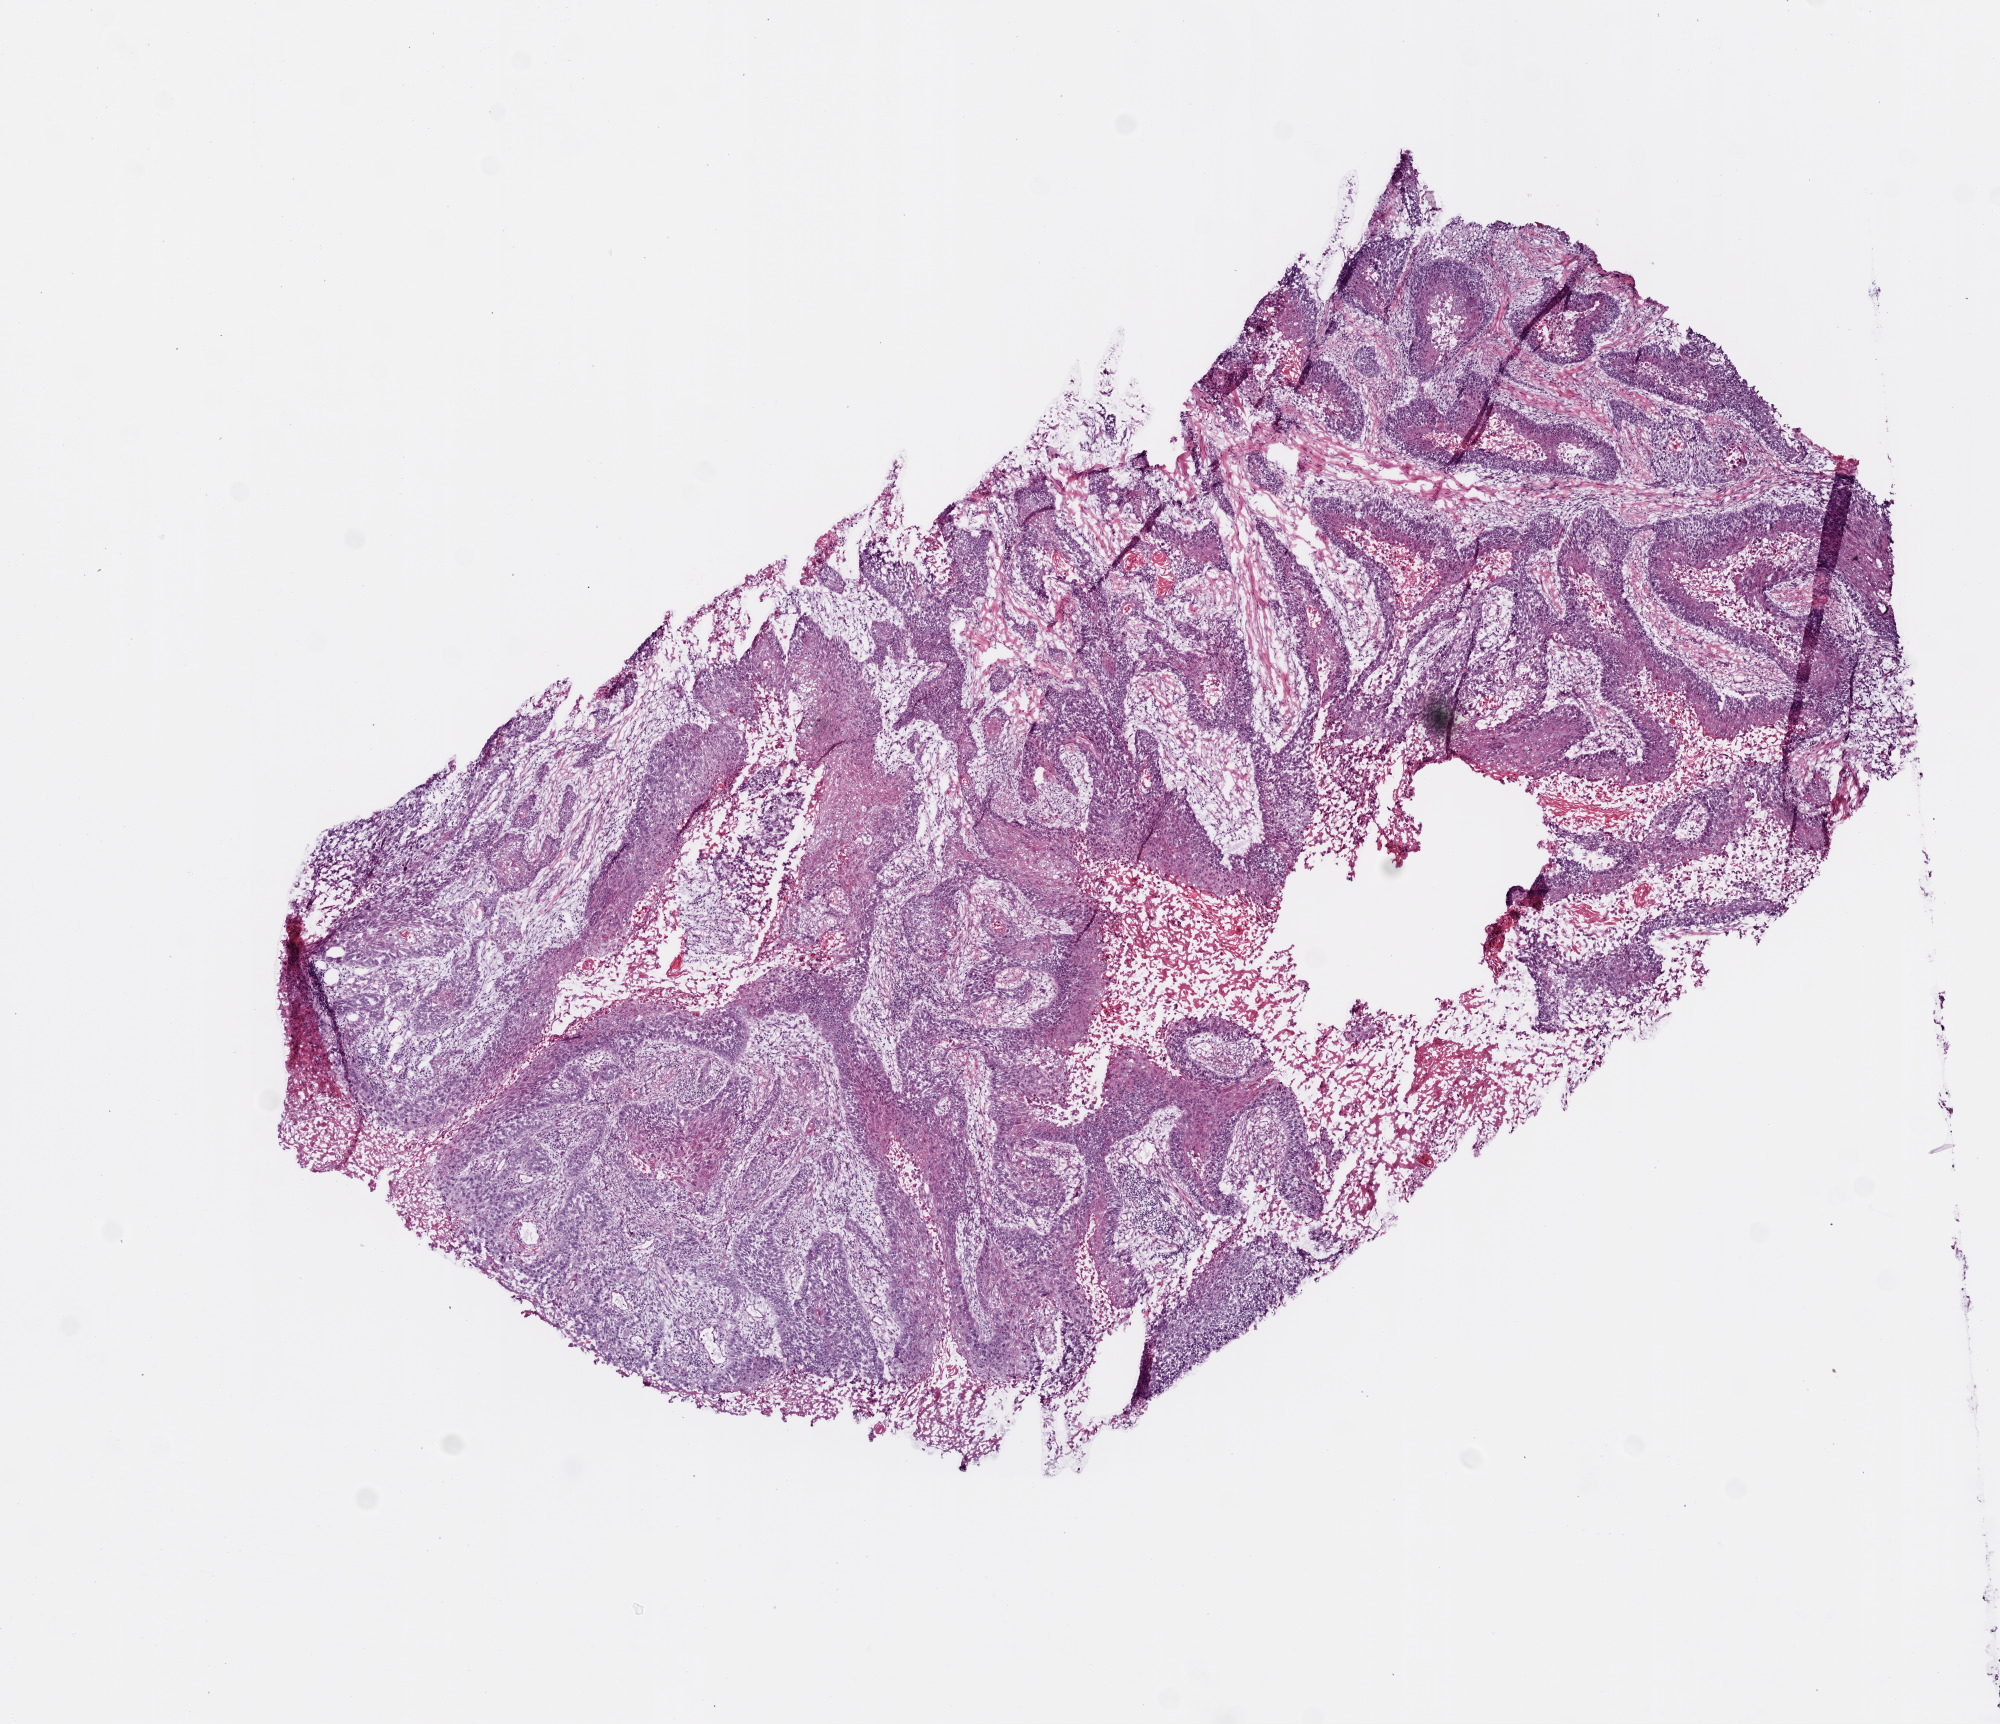
Whole-slide histology image, H&E-stained — a low-resolution overview of the entire scanned area, about 8.0 x 6.9 mm, frozen section from the top of the tissue portion, head and neck, primary tumour sample. Male patient; age at initial diagnosis 87 years. Histologic grade: G2 (moderately differentiated). Pathologist review of this section (percent, as recorded): tumour cells 90%, tumour nuclei 70%, normal cells 0%, stromal cells 0%, necrosis 10%. Infiltration values recorded for this section: lymphocyte infiltration 20%, monocyte infiltration 1%, neutrophil infiltration 5%.
* AJCC pathologic stage: III (6th edition)
* pathologic diagnosis: Squamous cell carcinoma, NOS (overlapping lesion of lip, oral cavity and pharynx)
* laterality: left